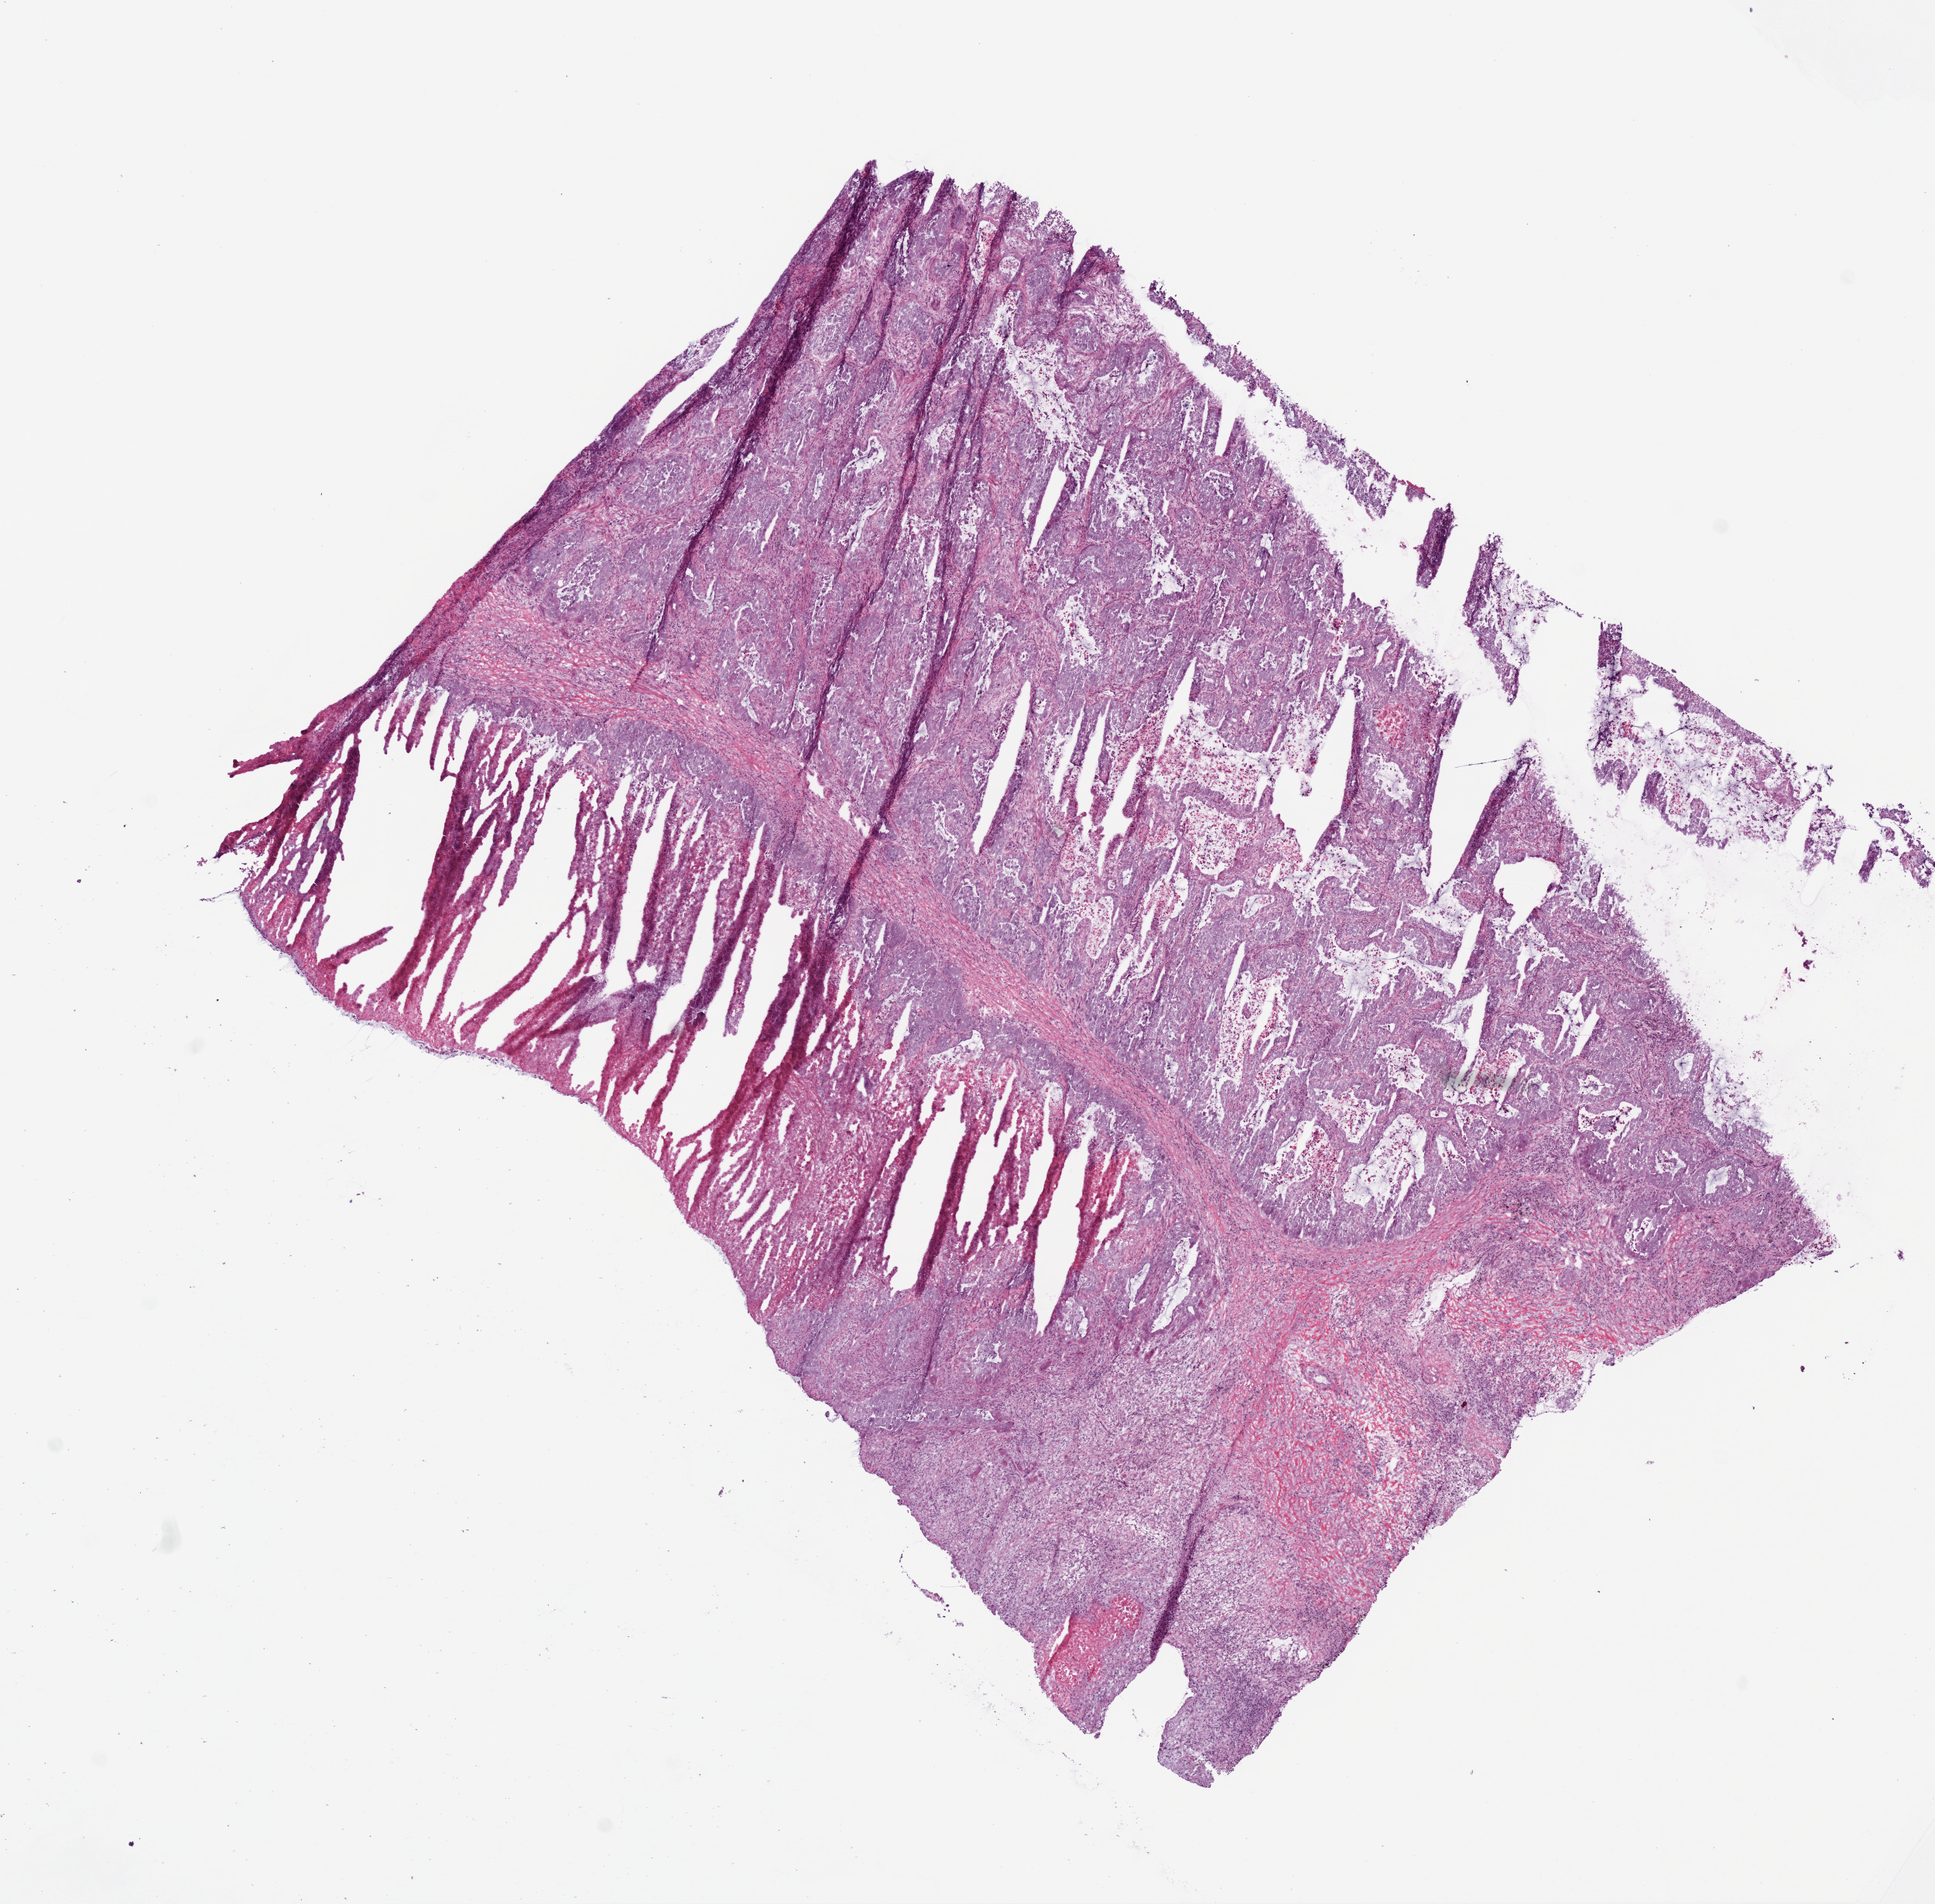
Whole-slide histology image, H&E-stained — shown as a low-resolution overview of the whole scanned area (about 10.0 x 9.9 mm, from a 20x scan); frozen section from the top of the tissue portion; sample: primary tumour, lung. Patient: male, age at initial diagnosis 63 years.
Histologic diagnosis: Acinar cell carcinoma.